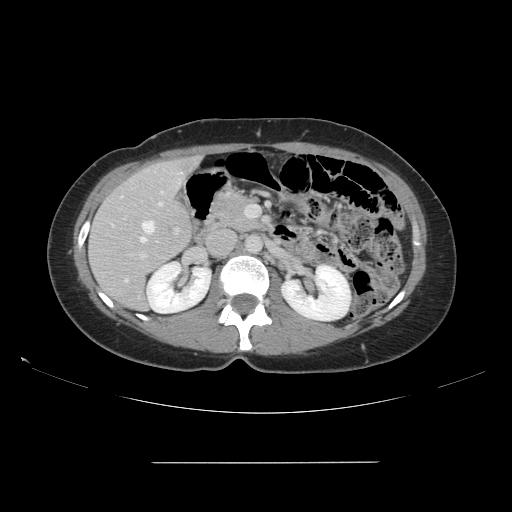
Contrast-enhanced abdominal CT, one axial slice. Position 78 of 151 along the scan axis. Intravenous contrast given. Soft-tissue window (W 400 / L 40 HU). 2.5 mm slice thickness. 512 × 512 image matrix, field of view 421 × 421 mm. Female patient, age 46 years. From the clinical record (not read from this slice): diagnosis: colorectal cancer liver metastases, imaged before liver resection; multiple liver metastases: yes; largest metastasis: 3 cm; disease in both lobes: yes.
Annotated regions visible in this slice (expert manual segmentation):
- hepatic veins: box from (x=121, y=196) to (x=155, y=243) px
- liver: (x=90, y=158)–(x=198, y=310)
- planned liver remnant (the part of the liver to remain after resection): (x=96, y=158)–(x=198, y=311)
- portal vein (with intrahepatic branches): (x=124, y=190)–(x=246, y=260)